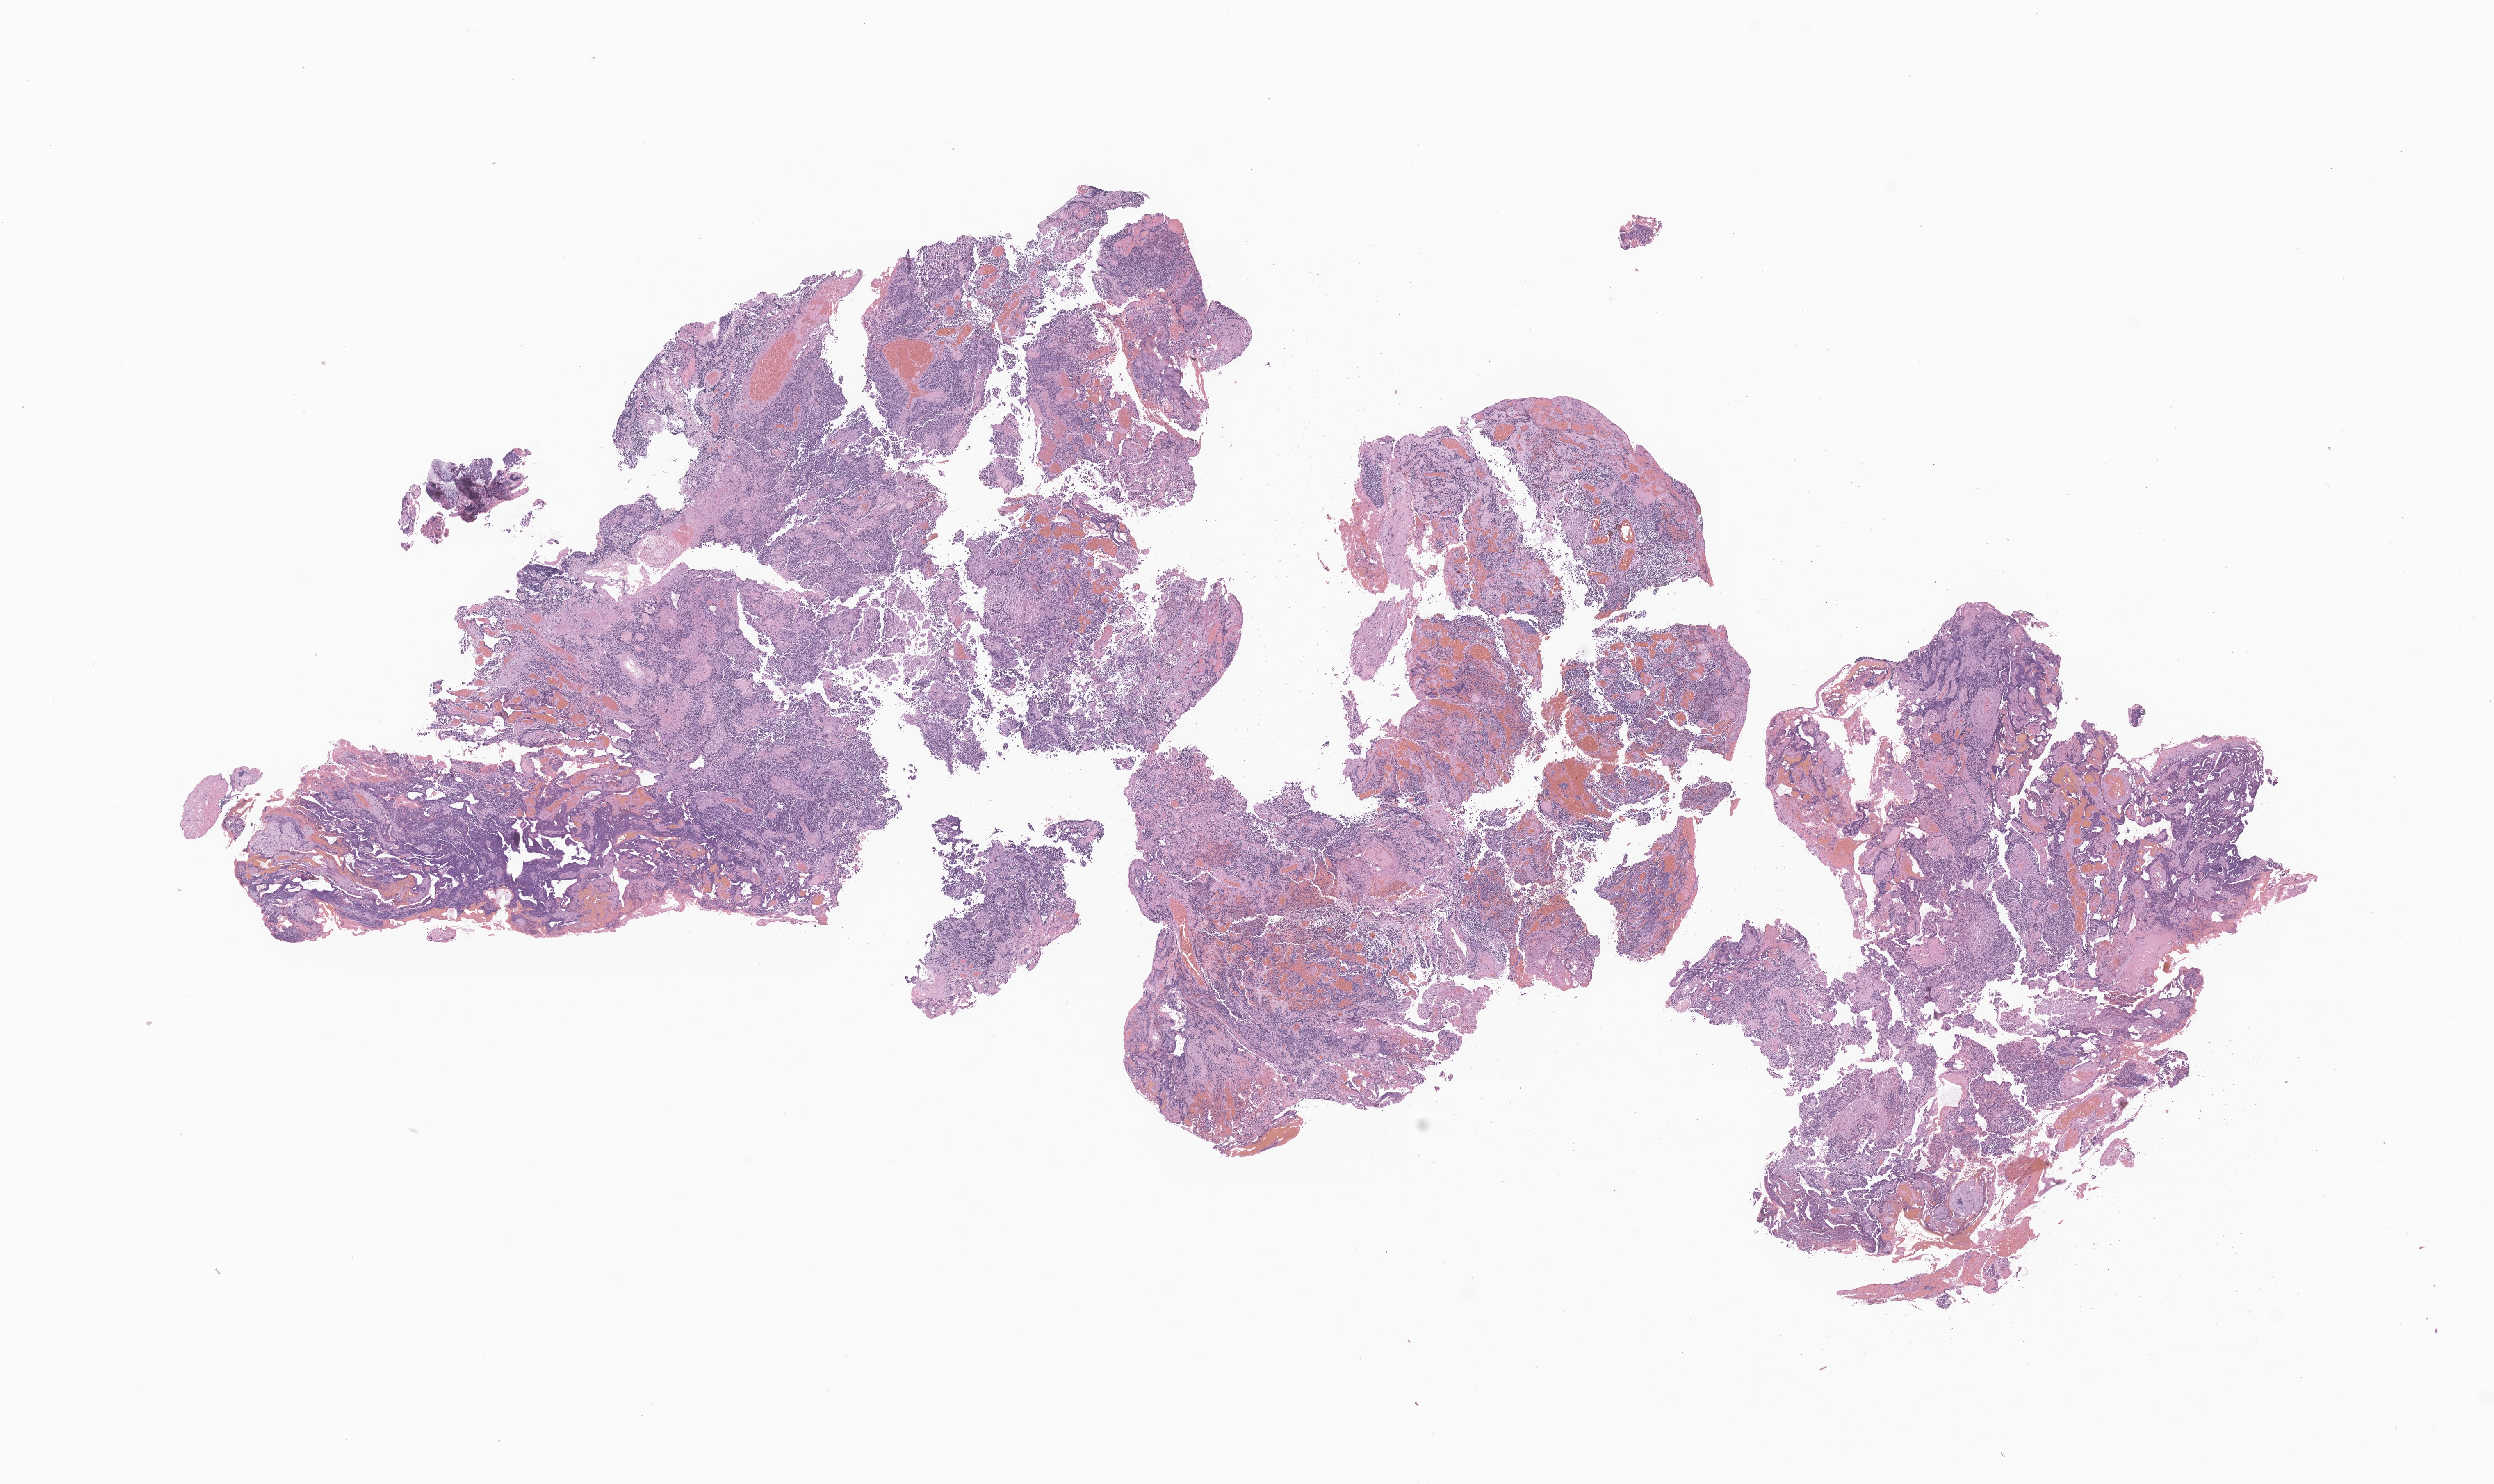
Digitized haematoxylin and eosin-stained section of tumor tissue from the brain — shown as a low-resolution overview of the whole scanned area (about 25.6 x 15.3 mm), FFPE section. Female patient, age 44 months.
- diagnosis: Neoplasm, uncertain whether benign or malignant